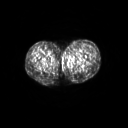
FDG PET of an extremity soft-tissue mass (from a PET/CT study), one axial slice; position 35 of 267 along the scan axis; 3.27 mm slice thickness; 128 × 128 image matrix, field of view 600 × 600 mm. Patient: female, 24 years. Case-level facts recorded for this patient, not image findings: histological type: leiomyosarcoma; grade: high; site of the primary tumour: groin.
Annotated regions visible in this slice (expert contour drawn on MRI and transferred to this co-registered scan by the dataset authors):
- gross tumour volume including surrounding oedema: bounding box [x1, y1, x2, y2] px = [62, 56, 69, 62]